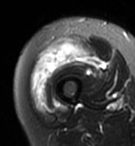
MRI of an extremity soft-tissue mass, one axial slice. Slice 22 of 95 in the series (ordered by position). T2-weighted fat-saturated. MR volume resampled by the dataset authors to the PET/CT grid (not the native acquisition matrix). 3.27 mm slice thickness. 135 × 146 image matrix, field of view 132 × 143 mm. Female patient. From the clinical record (not read from this slice): histological type: pleiomorphic undifferentiated sarcoma; grade: high; site of the primary tumour: right quadricep.
Annotated regions visible in this slice (expert contour drawn on MRI and transferred to this co-registered scan by the dataset authors):
- gross tumour volume including surrounding oedema: box from (x=30, y=43) to (x=90, y=110) px